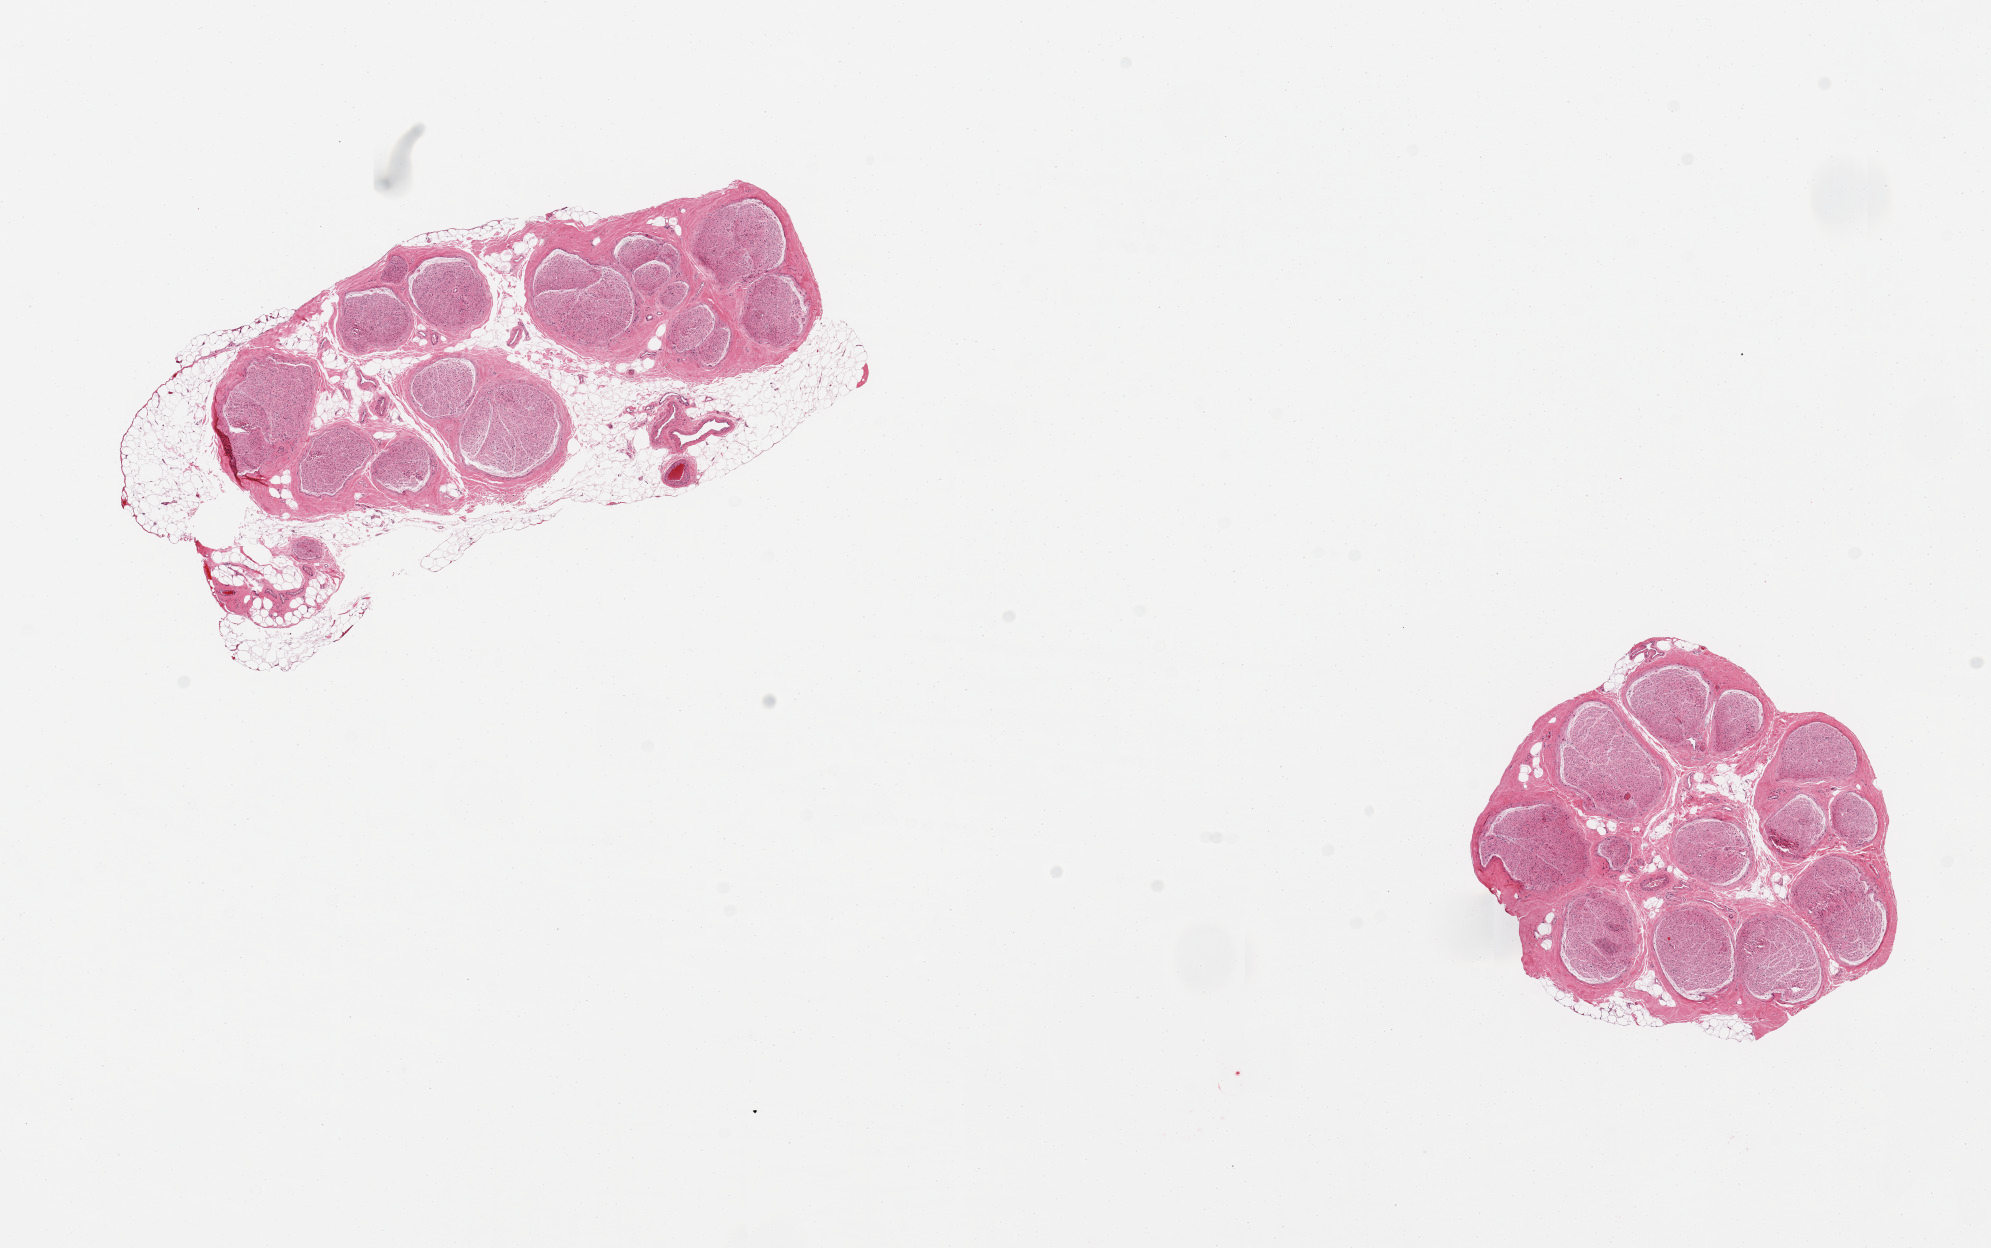
Haematoxylin and eosin whole-slide image — shown as a low-resolution overview of the whole scanned area (about 15.8 x 9.9 mm); PAXgene-fixed paraffin-embedded (PFPE) section; section of tibial nerve (target tissue); tissue donor sample. Donor sex: male.
Reviewer comment on this tissue sample: 2 pieces; one piece with adherent fat up to 1mm.